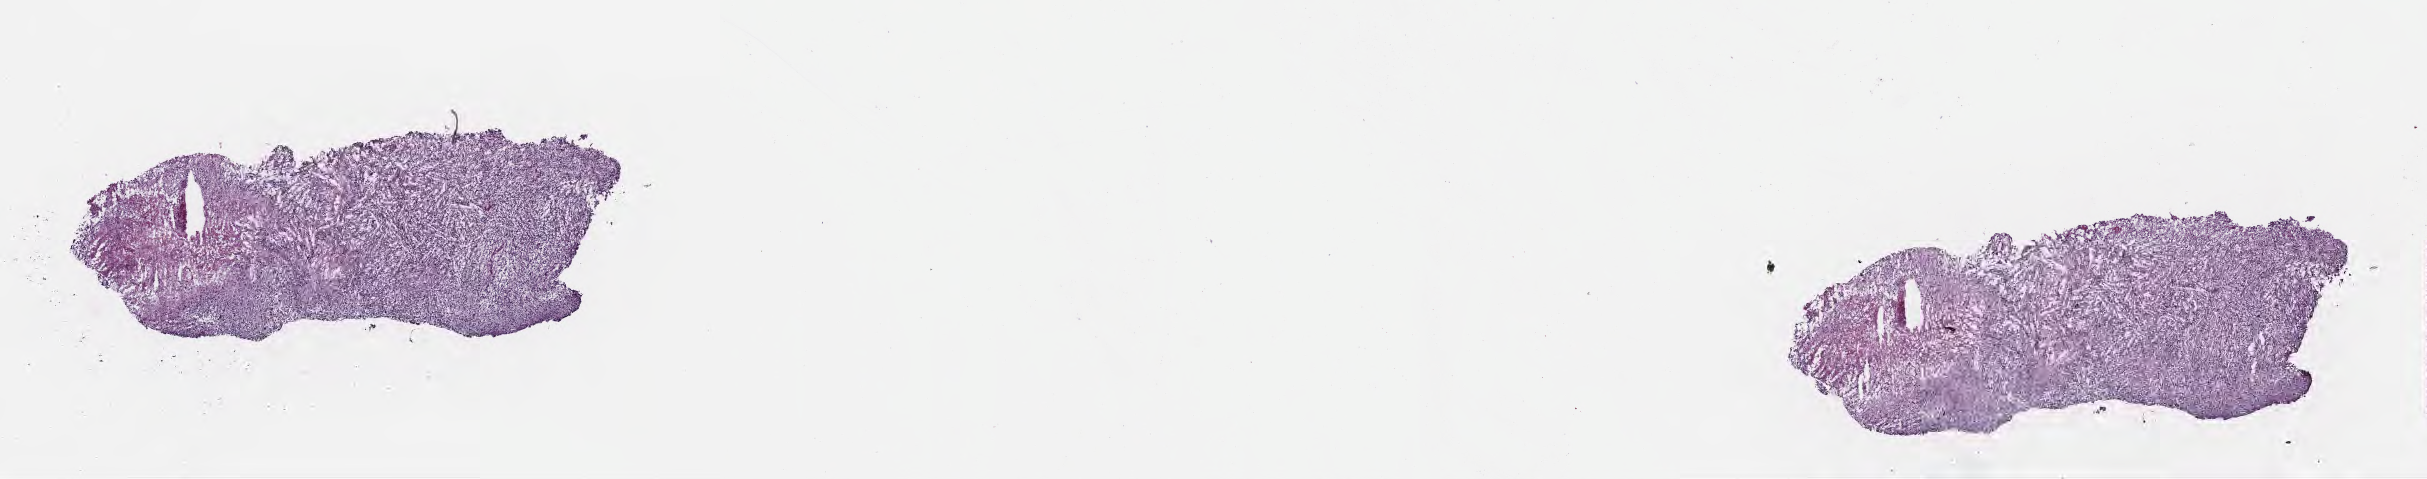
Whole-slide image, hematoxylin and eosin (H&E) stain, shown as a low-resolution overview of the whole scanned area (about 19.6 x 3.9 mm); frozen section; primary tumor; anatomic site: brain. Patient: female, age at initial diagnosis 50 years. Composition of this section per pathologist review: tumor cells 67%, tumor nuclei 88%, stromal cells 4%, necrosis 20%, normal cells 9%. Inflammatory infiltration, as recorded: lymphocyte infiltration 0%, monocyte infiltration 0%, neutrophil infiltration 0%.
Section: top of the tissue portion. Histologic diagnosis: Glioblastoma, NOS.